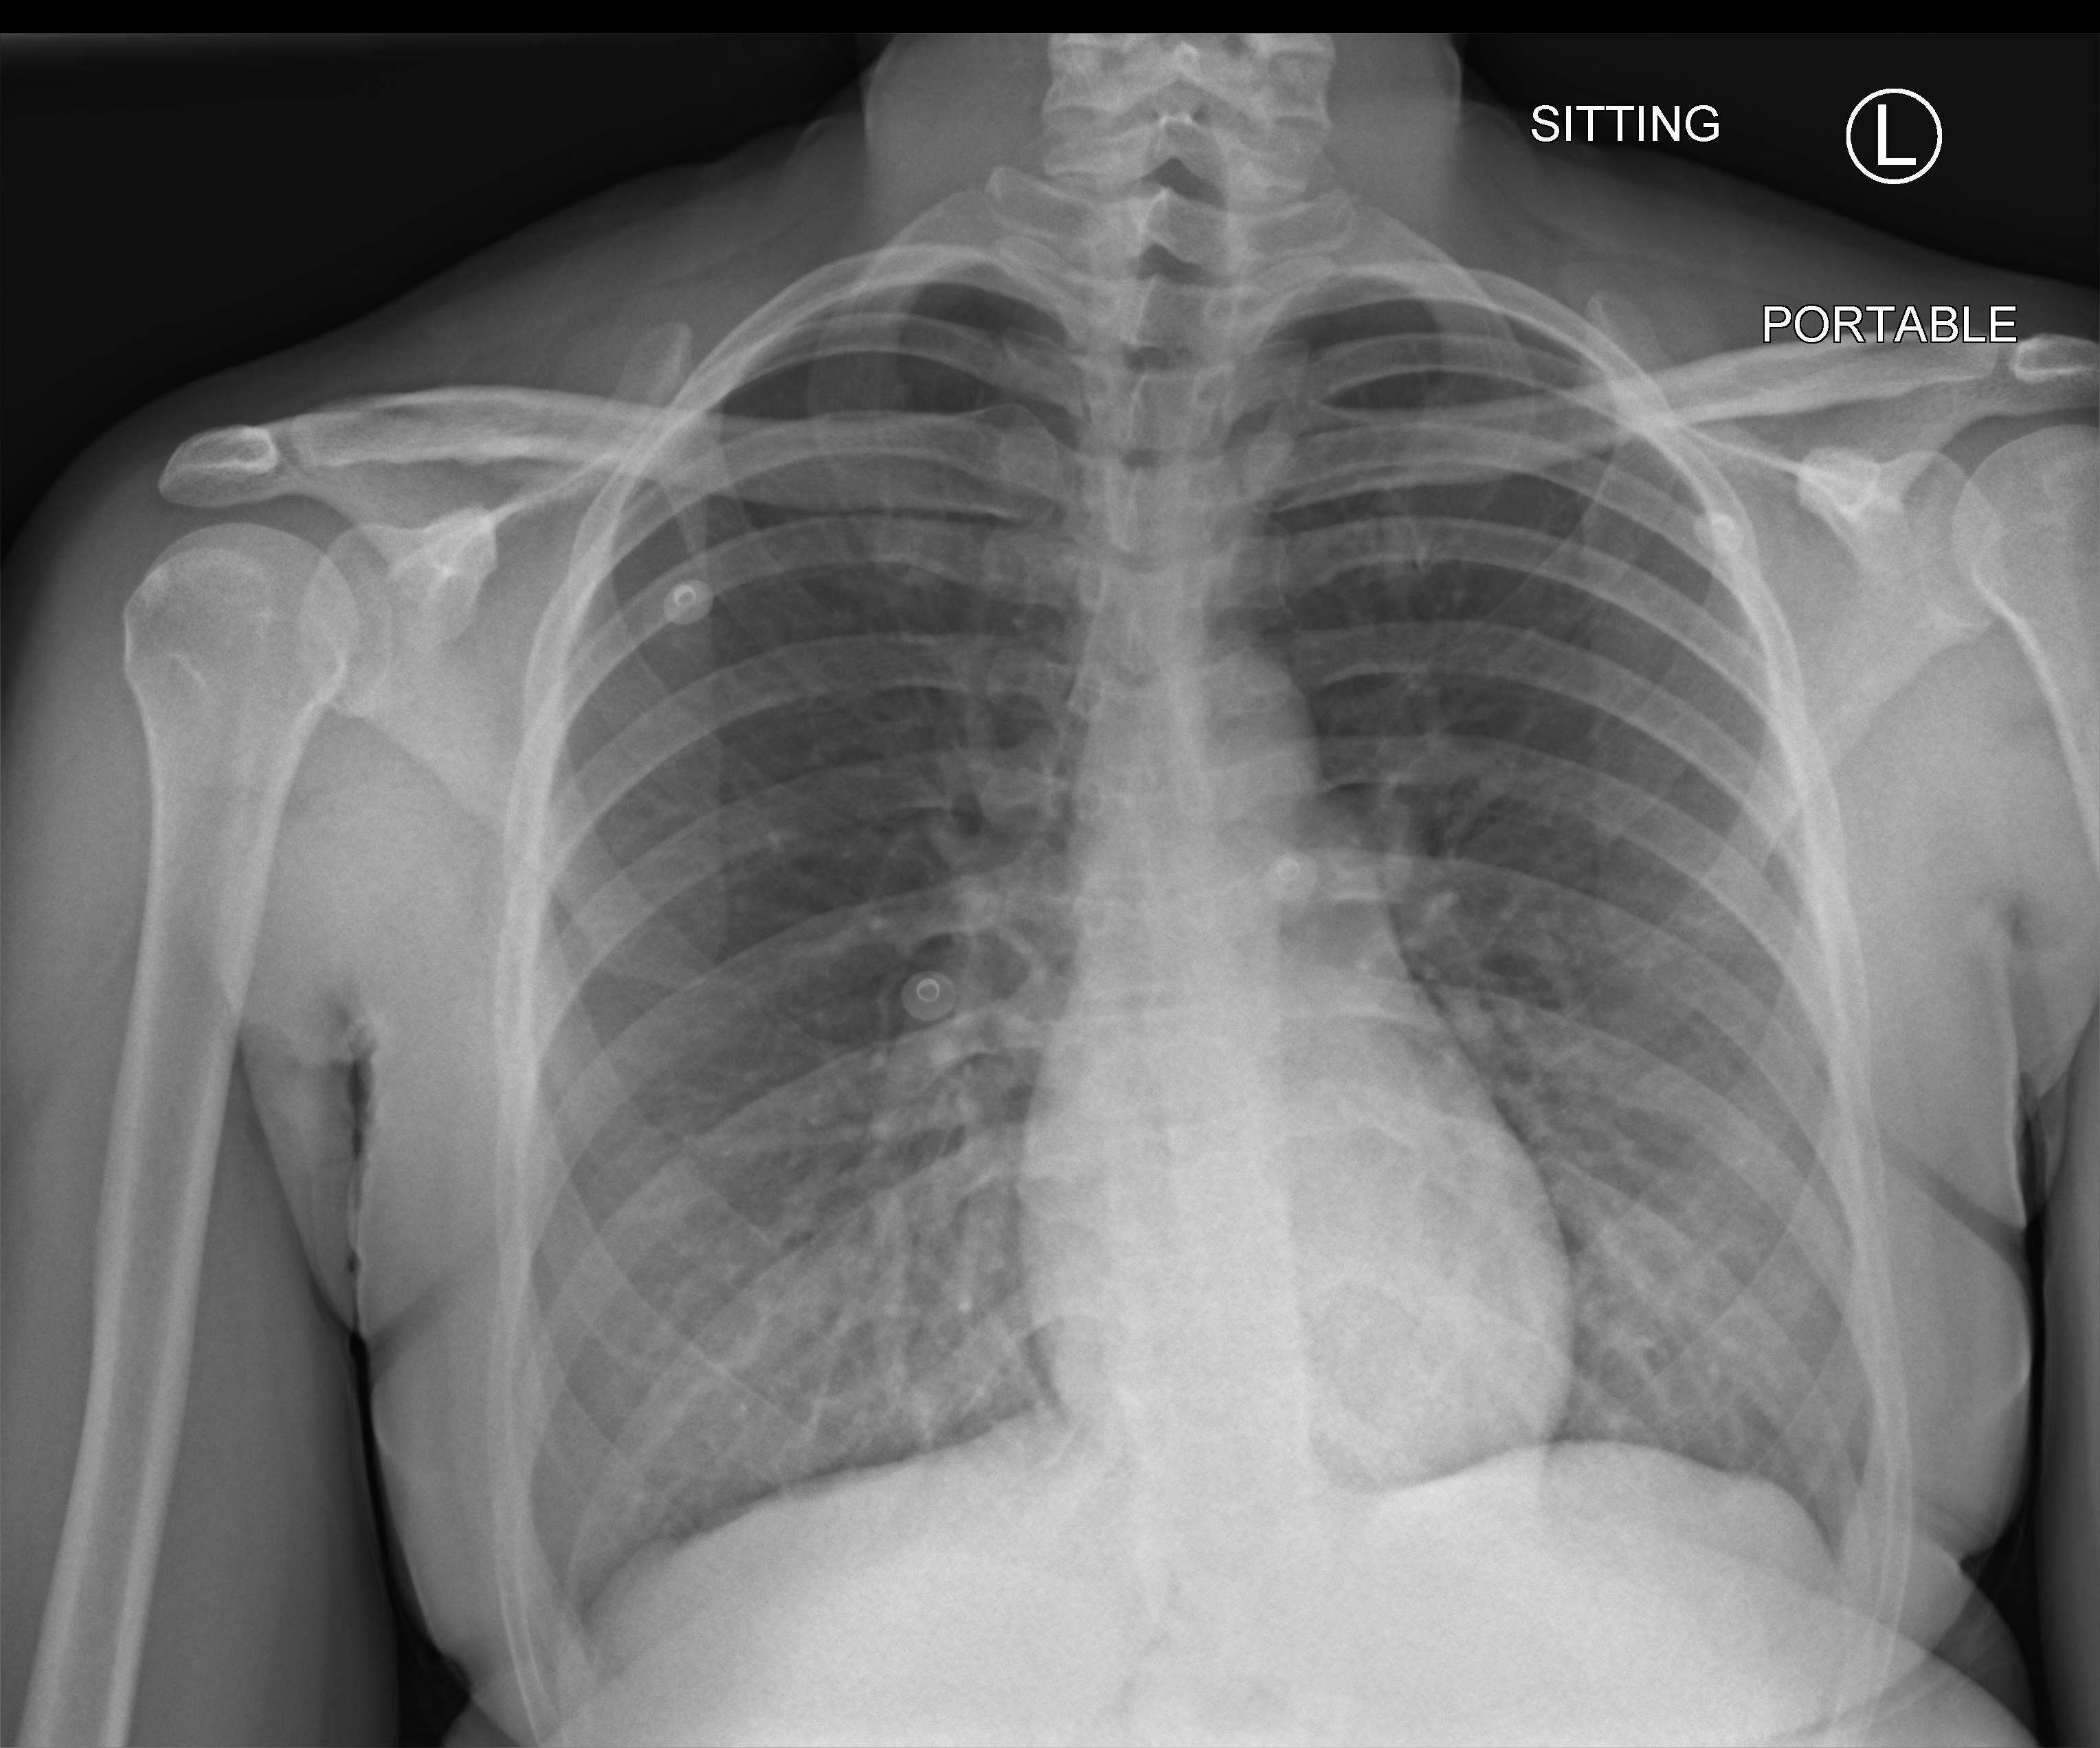
Portable chest radiograph, anteroposterior (AP) projection. Patient hospitalised with COVID-19; female, aged 18–59 years.
Hospital-stay facts (about this admission, not read from this image; timing relative to this image not recorded): hypertension (admission record): no.